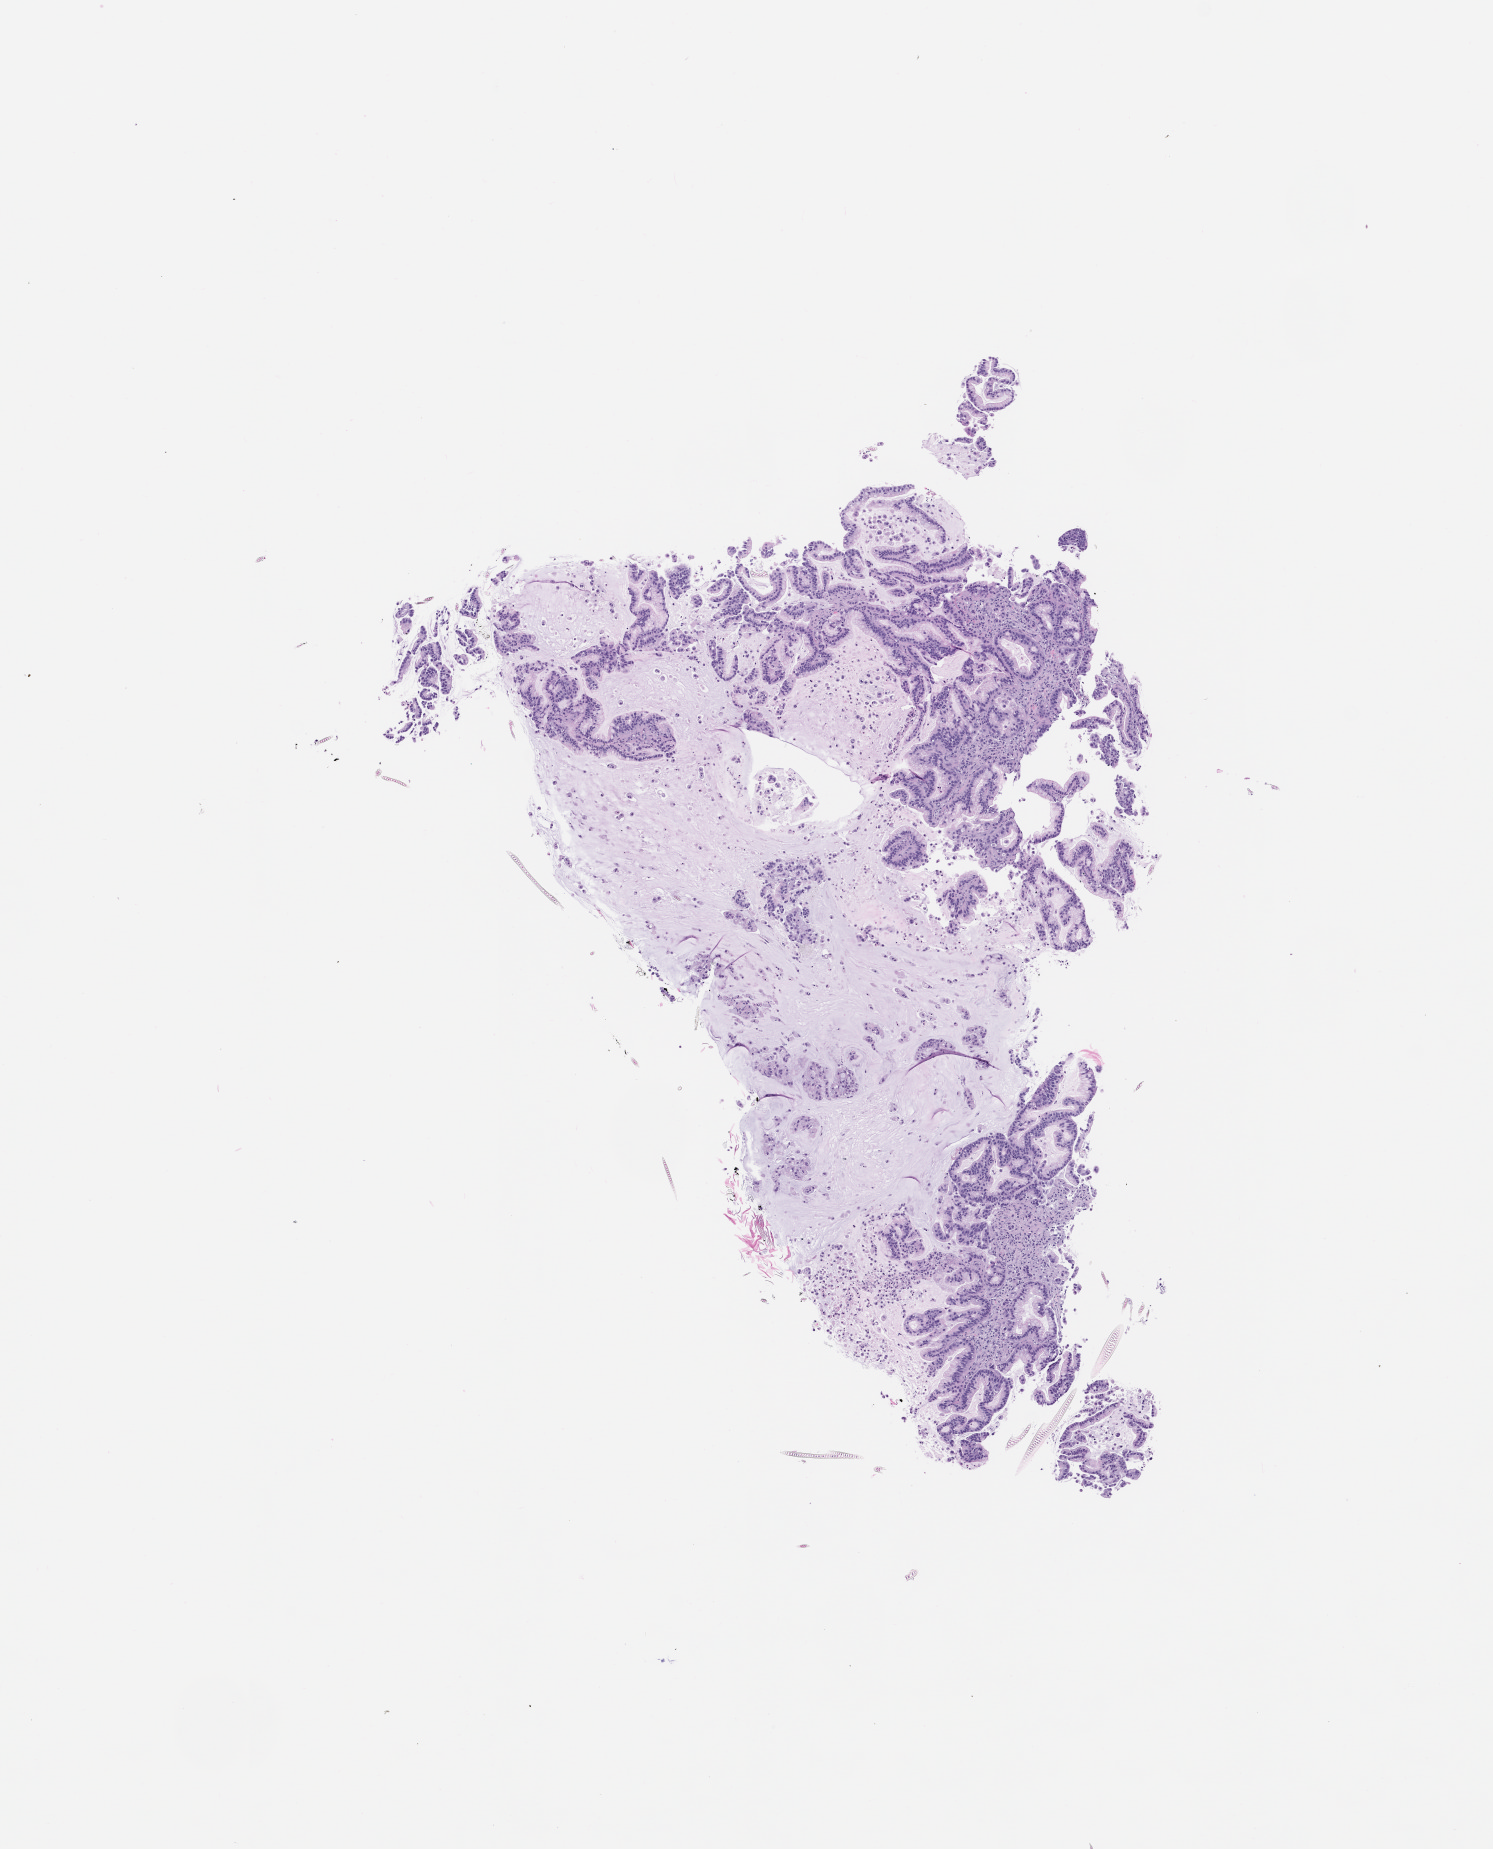
H&E whole-slide image of a patient-derived xenograft (PDX) tumor grown in a mouse, passage 1 — low-resolution overview of the scanned area, about 6.0 x 7.4 mm; FFPE section; originating tumor site category: pancreas.
• originating patient diagnosis: Pancreatic Adenocarcinoma